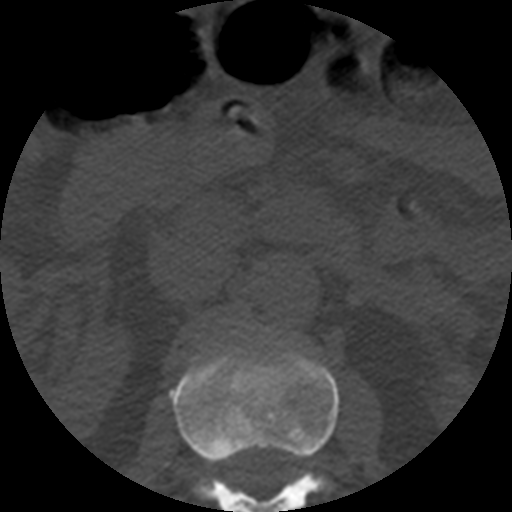
CT including the spine, one axial slice; slice 176 of 508 in the series (ordered by position); 120 kVp; bone window (W 1800 / L 400 HU); 1.25 mm slice thickness; 512 × 512 image matrix. Patient age 57 years. From the clinical record (not read from this slice): primary cancer: prostate.
Annotated regions visible in this slice (semi-automatic segmentation, software-assisted and operator-edited):
- L1 vertebra: bounding box (x1, y1, x2, y2) in pixels: (170, 346, 339, 512)